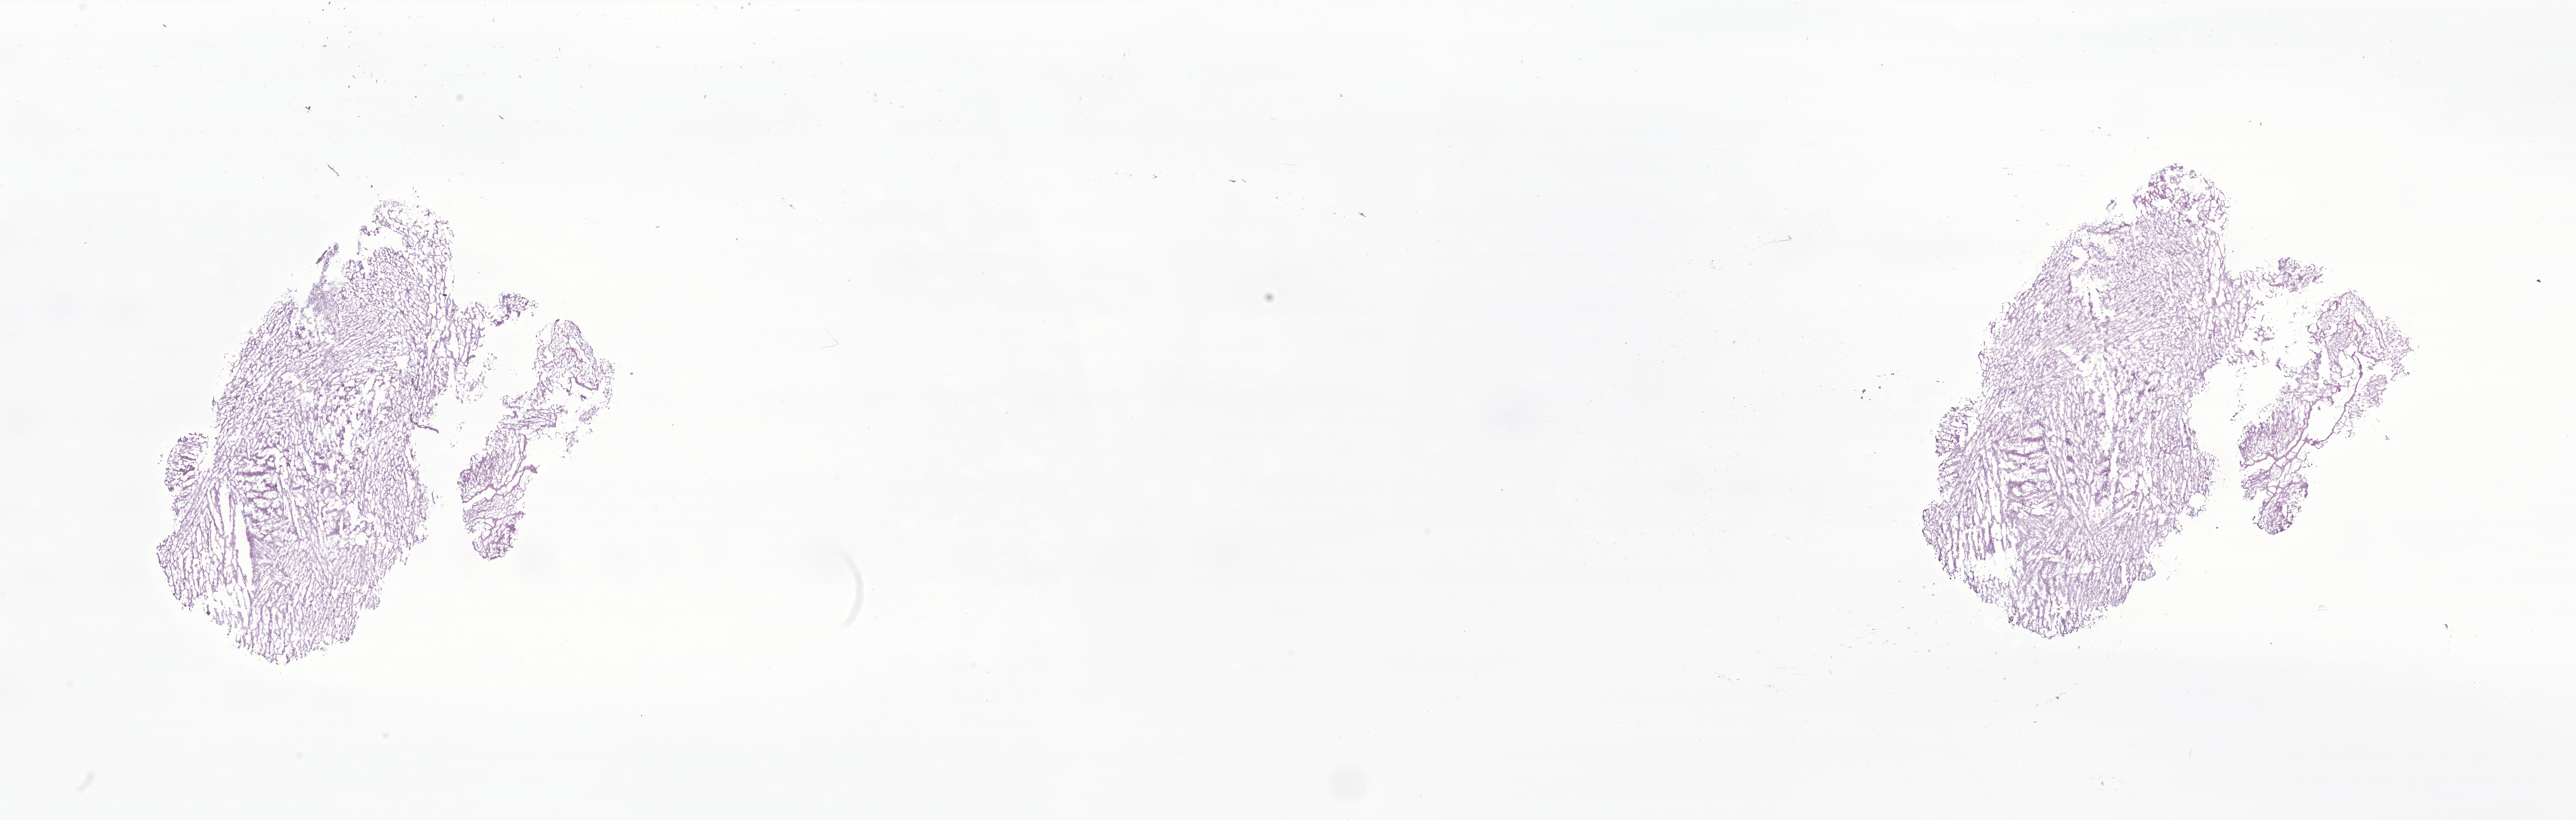
Whole-slide image, haematoxylin and eosin stain of tumor tissue from the brain, shown as a low-resolution overview of the whole scanned area (about 30.9 x 9.8 mm). Frozen section. Male patient, age 181 months (15 years 1 month).
Recorded diagnosis: Subependymal giant cell astrocytoma.